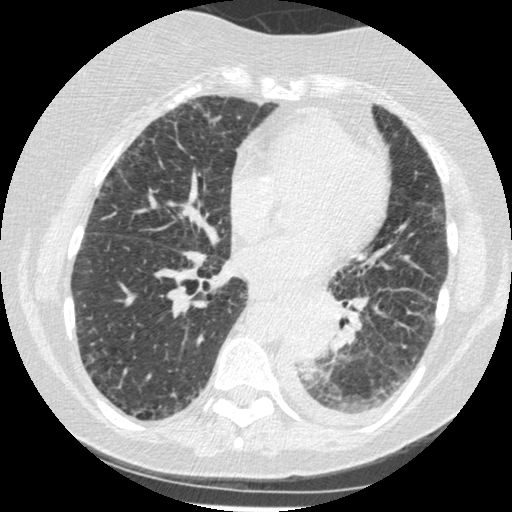
Axial slice from a low-dose chest CT screening exam. Third screening round (two years after baseline). Lung window (W 1500 / L -600 HU). Slice 244 of 341 in the series. 512 × 512 image matrix, field of view 310 × 310 mm. Female participant, aged 60 years at enrolment. Former smoker at enrolment.
• Lesion marked by an expert reader, box from (x=277, y=303) to (x=343, y=376) px.
• Screening reader's record for this exam (one nodule recorded; not confirmed to be the boxed lesion): non-calcified nodule or mass ≥4 mm, left lower lobe, 54 × 38 mm, smooth margins, soft tissue attenuation, pre-existing on the prior screen: yes; interval growth: yes.
• Participant outcome: lung cancer diagnosed 15 days after this screen — small cell carcinoma, NOS, left lower lobe, undifferentiated (G4), stage IV (AJCC 6th edition), 69 mm at pathology.